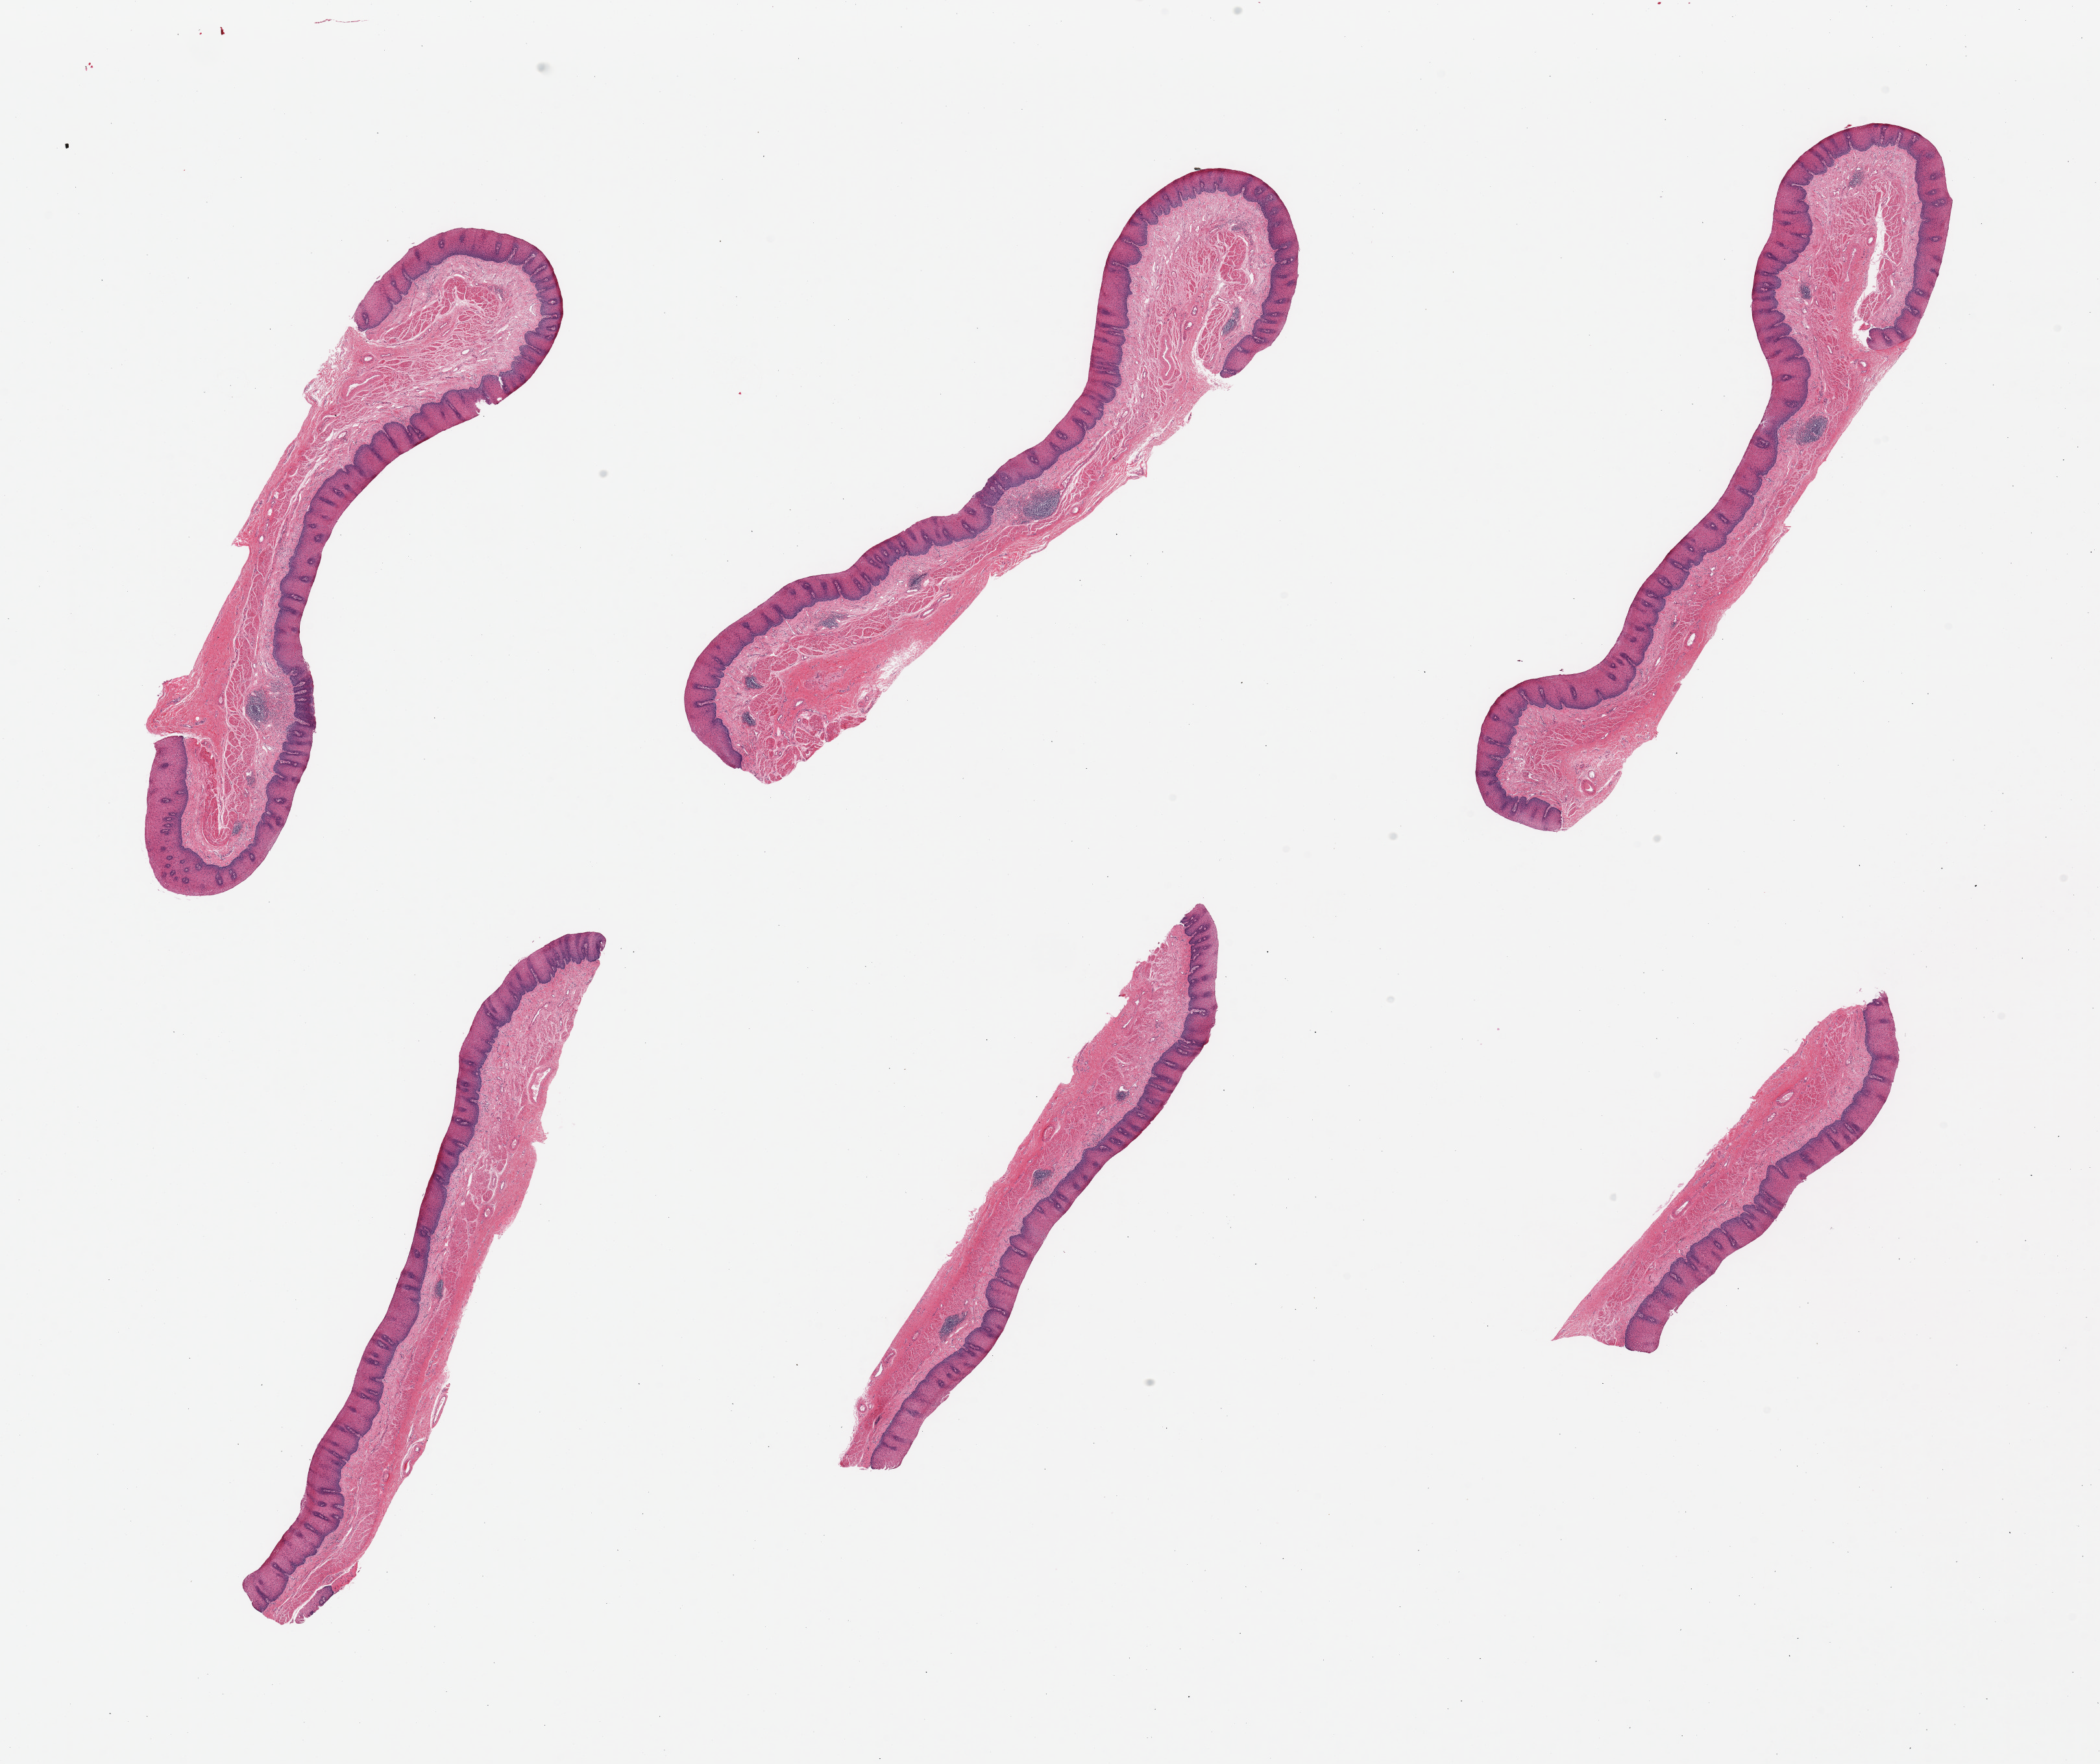
Digitized haematoxylin and eosin-stained section, a low-resolution overview of the entire scanned area, about 25.6 x 21.5 mm (acquisition: 20x scan); PAXgene-fixed, paraffin-embedded tissue; section of esophageal mucous membrane (target tissue); donor tissue sample.
• reviewer comment on this tissue sample: 6 pieces